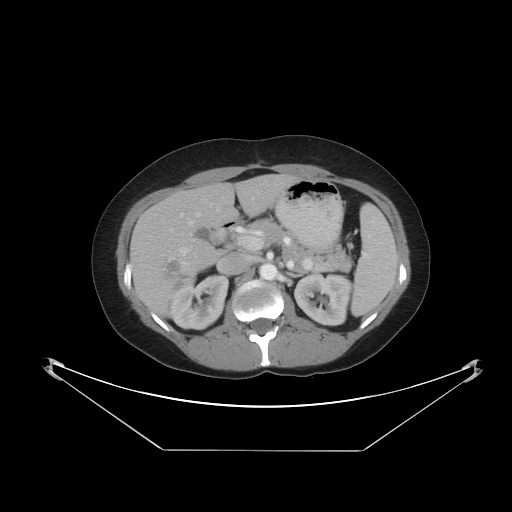
Contrast-enhanced abdominal CT, one axial slice. 120 kVp. Soft-tissue window (W 400 / L 40 HU). 5 mm slice thickness. 512 × 512 image matrix, field of view 482 × 482 mm. Female patient, age 38 years. Case-level facts recorded for this patient, not image findings: diagnosis: colorectal cancer liver metastases, imaged before liver resection; multiple liver metastases: yes; largest metastasis: 2.5 cm; disease in both lobes: no.
Annotated regions visible in this slice (manually delineated by an expert):
- hepatic veins: bounding box <188,212,200,225> (left, top, right, bottom; pixels)
- liver: <130,175,297,316>
- planned liver remnant (the part of the liver to remain after resection): <166,174,297,229>
- portal vein (with intrahepatic branches): <168,208,220,265>
- liver metastasis: <168,262,182,277>